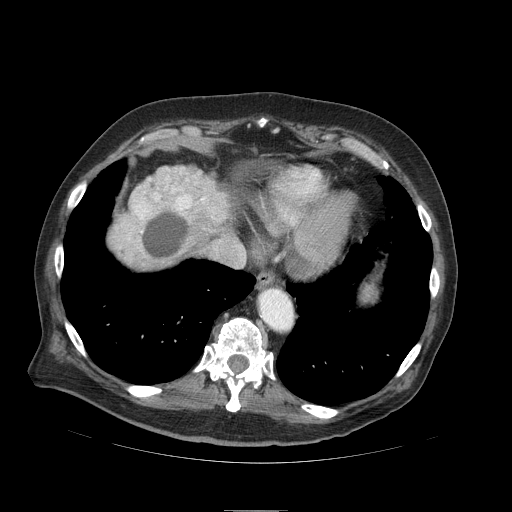
Contrast-enhanced abdominal CT (liver protocol), one axial slice. Position 81 of 103 along the scan axis. Reconstruction kernel STANDARD. 120 kVp. Soft-tissue window (W 400 / L 40 HU). 512 × 512 image matrix, field of view 440 × 440 mm. Case-level facts recorded for this patient, not image findings: diagnosis: hepatocellular carcinoma (patient treated with transarterial chemoembolisation; whether this scan precedes or follows treatment is not stated here); TNM stage (as recorded): Stage-IIIA.
Outlined on this slice (semi-automatic segmentation, software-assisted and operator-edited):
- liver parenchyma outside the tumour (the mass and vessels are separate outlines, so this box may not span the whole liver): box from (x=108, y=166) to (x=230, y=270) px
- mass: (x=115, y=167)–(x=227, y=259)